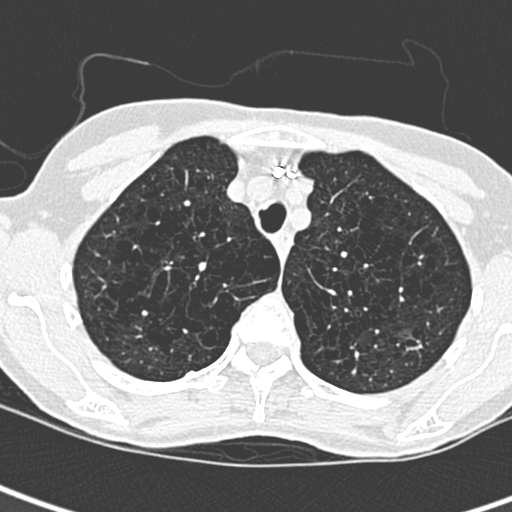
Low-dose screening chest CT, axial slice; baseline annual screen; lung window (W 1500 / L -600 HU); 1.3 mm slice thickness; lung (sharp) reconstruction kernel (D); 120 kVp; slice 55 of 259 in the series. Female participant, aged 71 years at enrolment.
Expert-annotated lung lesion, bounding box [x1, y1, x2, y2] px = [397, 329, 436, 366]. Screening reader's record for this exam: no non-calcified nodule ≥4 mm recorded. Official screen result: negative screen, no significant abnormalities. Later outcome: lung cancer diagnosed 975 days after this screen (after the third annual screen) — adenocarcinoma, NOS, left upper lobe, moderately differentiated (G2), stage IA (AJCC 6th edition), 12 mm at pathology.